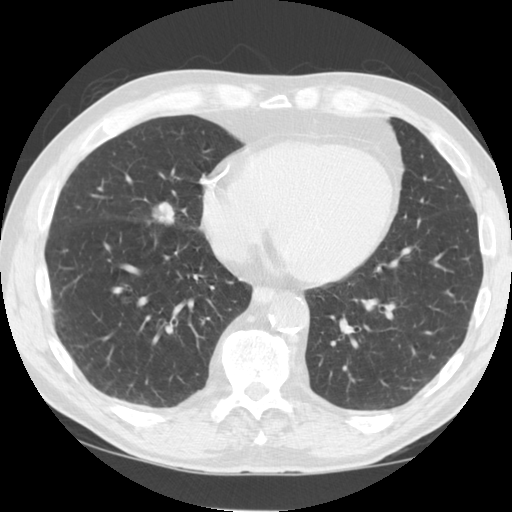
Axial slice from a low-dose chest CT screening exam. Third annual screen. Lung window (W 1500 / L -600 HU). 2.5 mm slice thickness. 120 kVp. Slice 87 of 125 in the series. Male, age 64 years at enrolment.
Expert-annotated lung lesion, bounding box (x1, y1, x2, y2) in pixels: (129, 186, 206, 240). Reader record for this screening exam (exam-level; its link to the box is not recorded): non-calcified nodule or mass ≥4 mm, right middle lobe, 21 × 14 mm, smooth margins, soft tissue attenuation, pre-existing on the prior screen: yes; interval growth: yes. Participant outcome: lung cancer diagnosed 74 days after this screen — non-small cell carcinoma, right middle lobe, poorly differentiated (G3), stage IIIA (AJCC 6th edition), 20 mm at pathology.